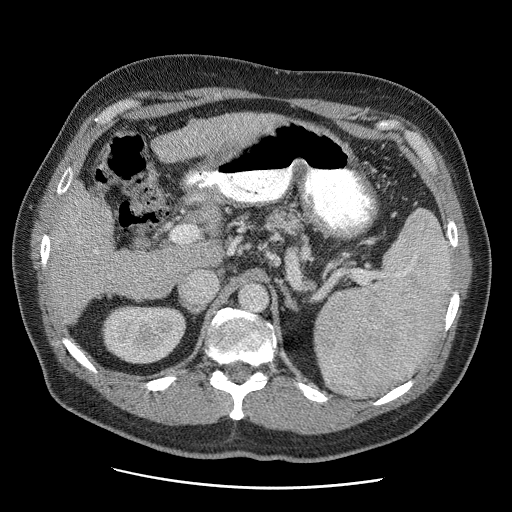
Contrast-enhanced abdominal CT (liver protocol), one axial slice. Slice 24 of 81 in the series (ordered by position). Soft-tissue window (W 400 / L 40 HU). 2.5 mm slice thickness. 512 × 512 image matrix, field of view 380 × 380 mm. Case-level facts recorded for this patient, not image findings: diagnosis: hepatocellular carcinoma (patient treated with transarterial chemoembolisation; whether this scan precedes or follows treatment is not stated here); TNM stage (as recorded): Stage-IIIA; Child-Pugh class: A; tumour nodularity: multinodular; tumour size: 5.5 cm.
Structures marked on this image (semi-automatic segmentation, software-assisted and operator-edited):
- abdominal aorta: bounding box (x1, y1, x2, y2) in pixels: (240, 285, 268, 312)
- liver parenchyma outside the tumour (the mass and vessels are separate outlines, so this box may not span the whole liver): (50, 112, 286, 322)